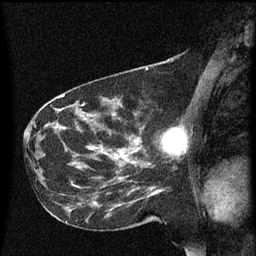
Breast MRI (dynamic contrast-enhanced), one sagittal slice. Slice 30 of 60 in the series (ordered by position). Dynamic contrast-enhanced series, image 2 of 3 at this slice position (ordered by acquisition). 1.5 T. TE 4.2 ms, TR 8.4 ms. 256 × 256 image matrix. Female patient, age 41 years. Case-level facts recorded for this patient, not image findings: setting: breast cancer imaged before/during neoadjuvant chemotherapy; receptor status: triple-negative.
Outlined on this slice (semi-automatic segmentation, software-assisted and operator-edited):
- analysis volume of interest (the breast-tissue region the enhancement analysis was run in; not a lesion): bounding box [x1, y1, x2, y2] px = [138, 128, 187, 167]
- tumour enhancement mask (voxels above the 70 % enhancement threshold inside the analysis volume of interest): [163, 130, 185, 153]